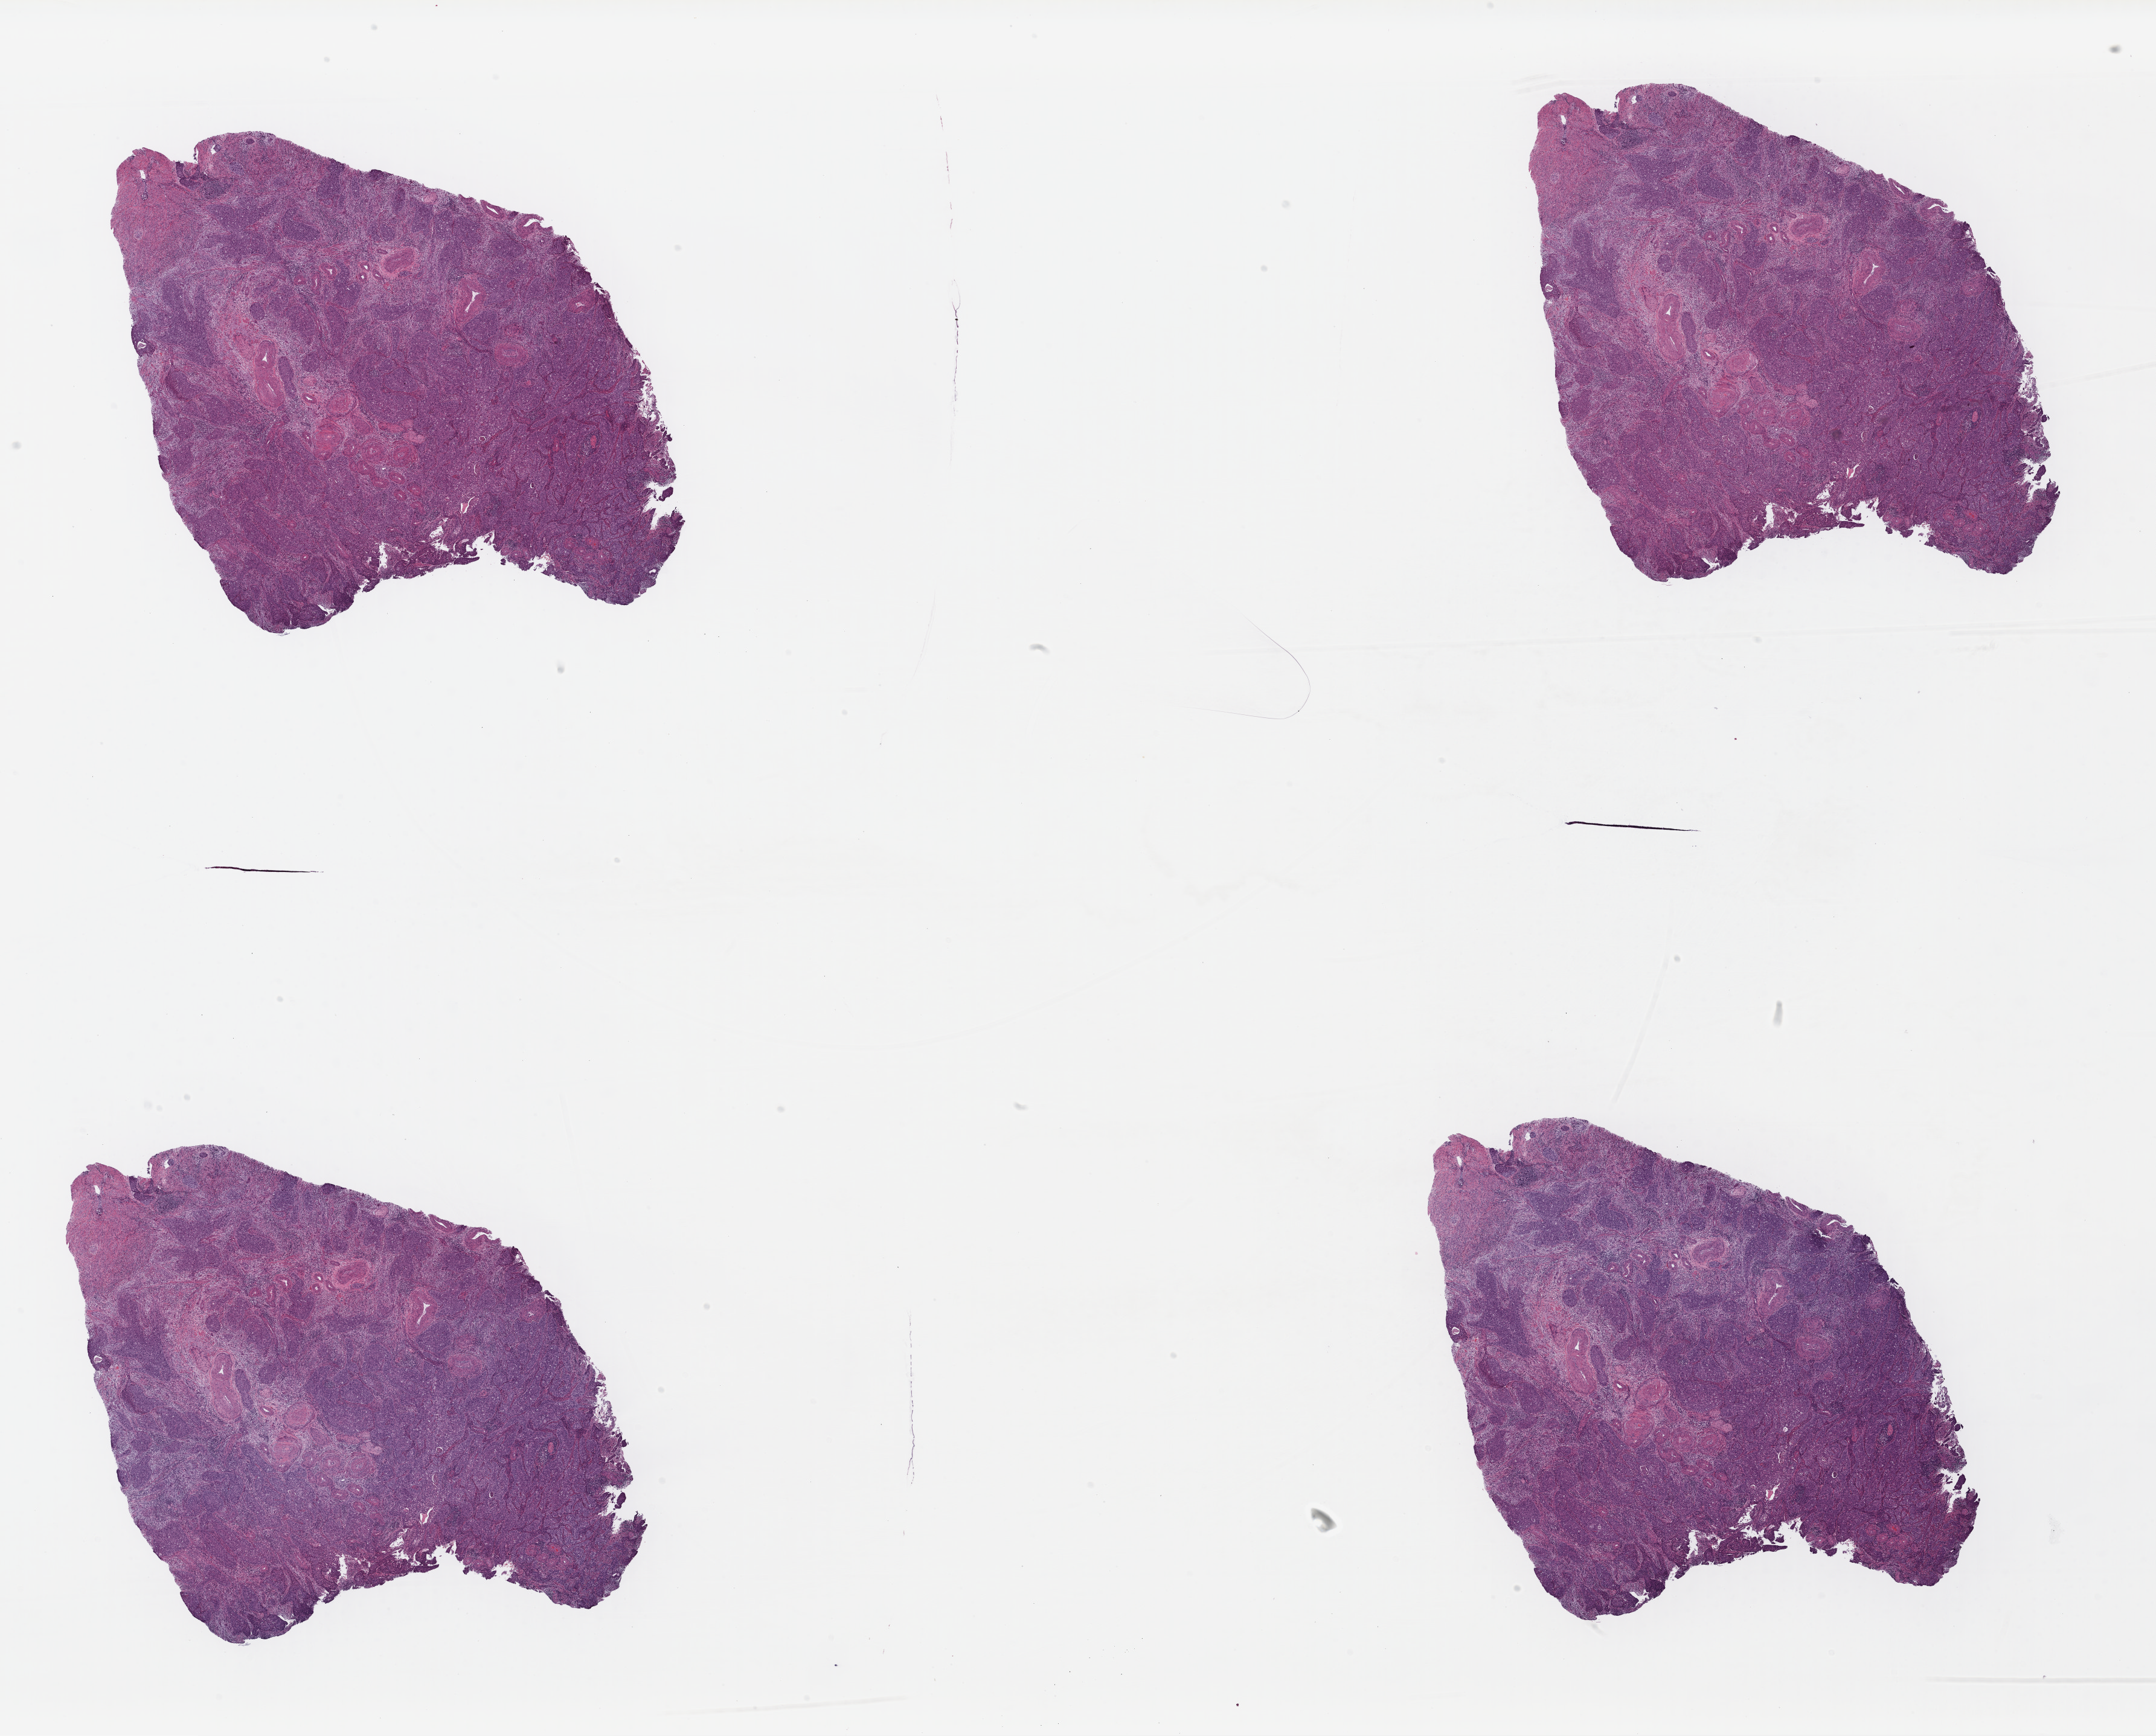
Digitized H&E tissue section (whole slide) — low-resolution overview of the scanned area, about 28.1 x 22.6 mm (acquisition: 40x scan); FFPE section; primary tumour sample from the cervix. Patient: female, age at initial diagnosis 40 years.
Histologic diagnosis: Squamous cell carcinoma, NOS.